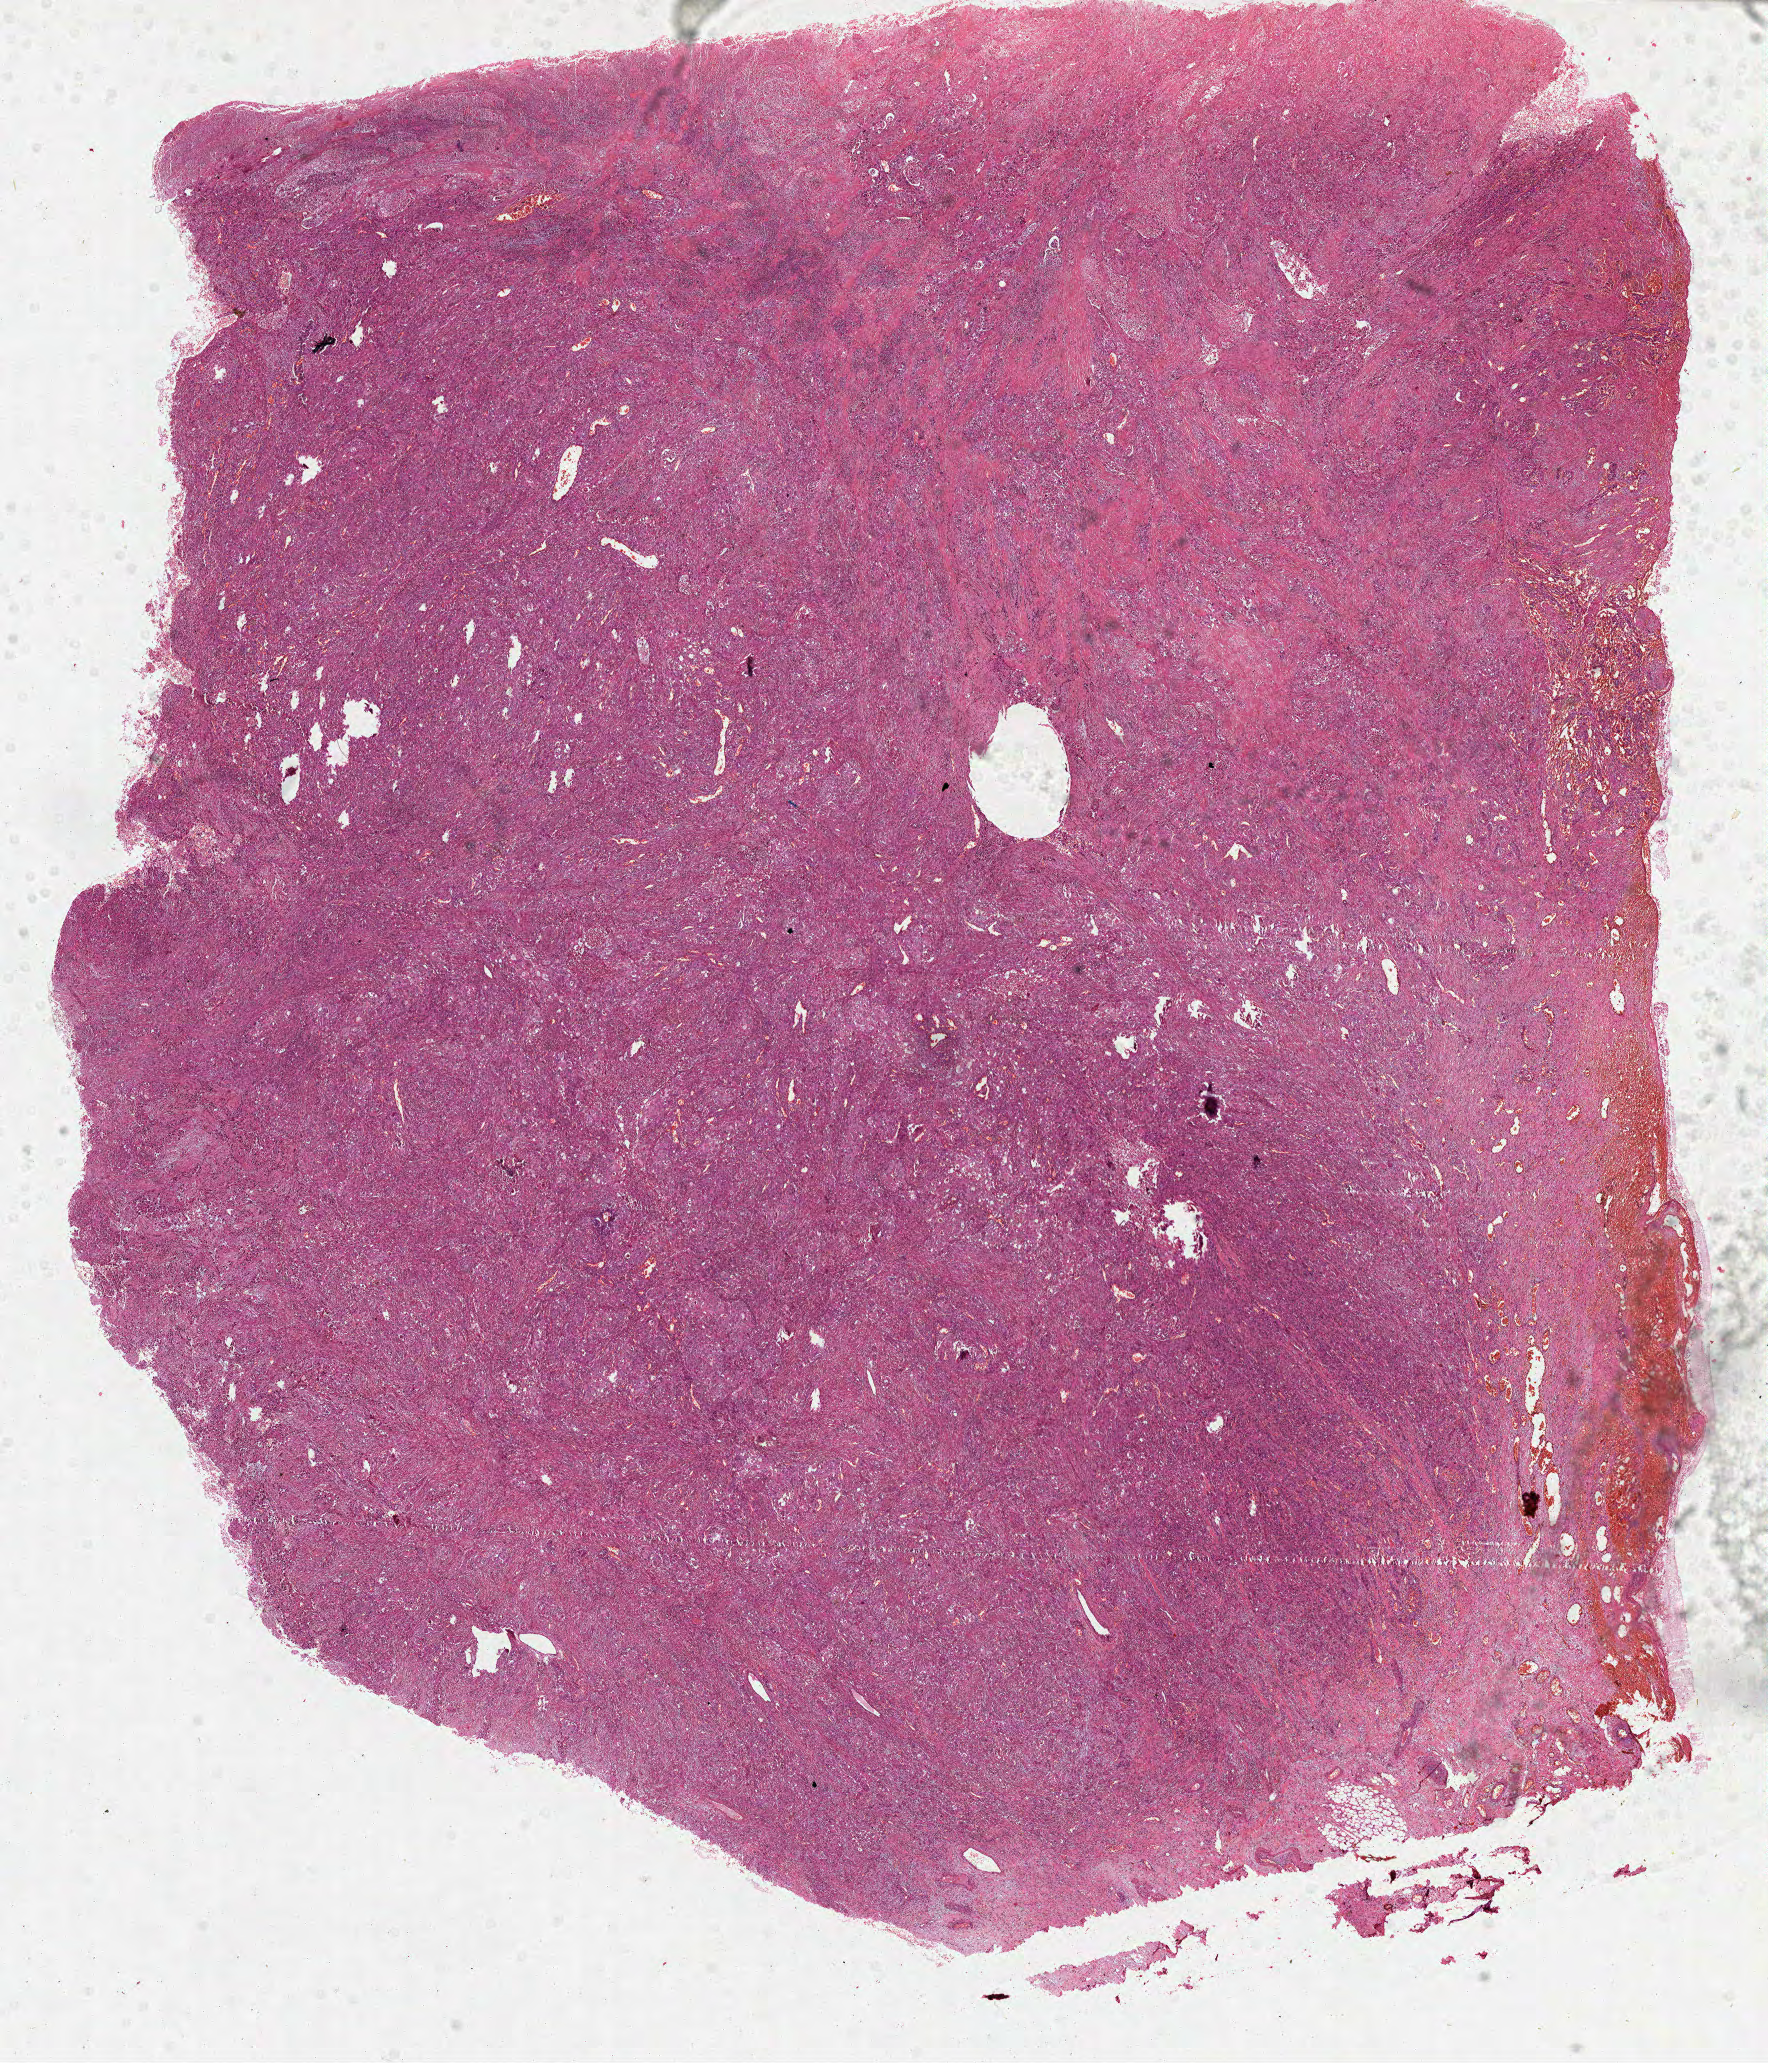
Digitized H&E-stained tissue section (whole slide) — whole scanned area (about 14.3 x 16.6 mm, from a 40x scan) shown as a low-resolution overview; formalin-fixed paraffin-embedded (FFPE) diagnostic section; sample: primary tumour, lung. Patient: male, age at initial diagnosis 47 years.
Histologic diagnosis: Squamous cell carcinoma, NOS (upper lobe, lung). AJCC pathologic stage: IIIA.